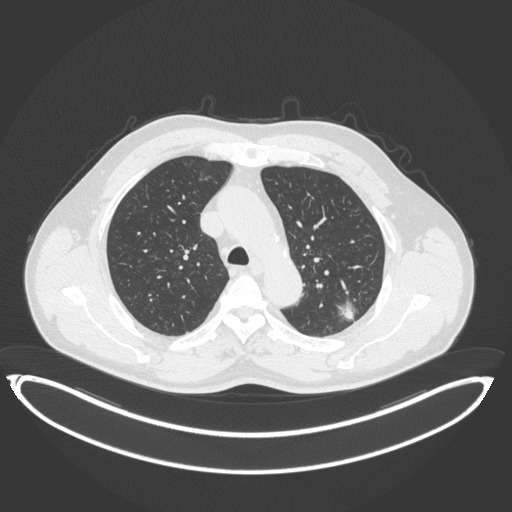
Chest CT, one axial slice. Slice 262 of 399 in the series (ordered by position). 120 kVp. Lung window (W 1500 / L -600 HU). 1 mm slice thickness. 512 × 512 image matrix, field of view 469 × 469 mm. Patient: male, 58 years. From the clinical record (not read from this slice): clinical TNM (as recorded): T1c N0 M0; histopathological grade: G1-2.
Annotated regions visible in this slice (rectangle marked by the reading radiologist):
- lung tumour (recorded histology: adenocarcinoma): box from (x=335, y=296) to (x=365, y=323) px